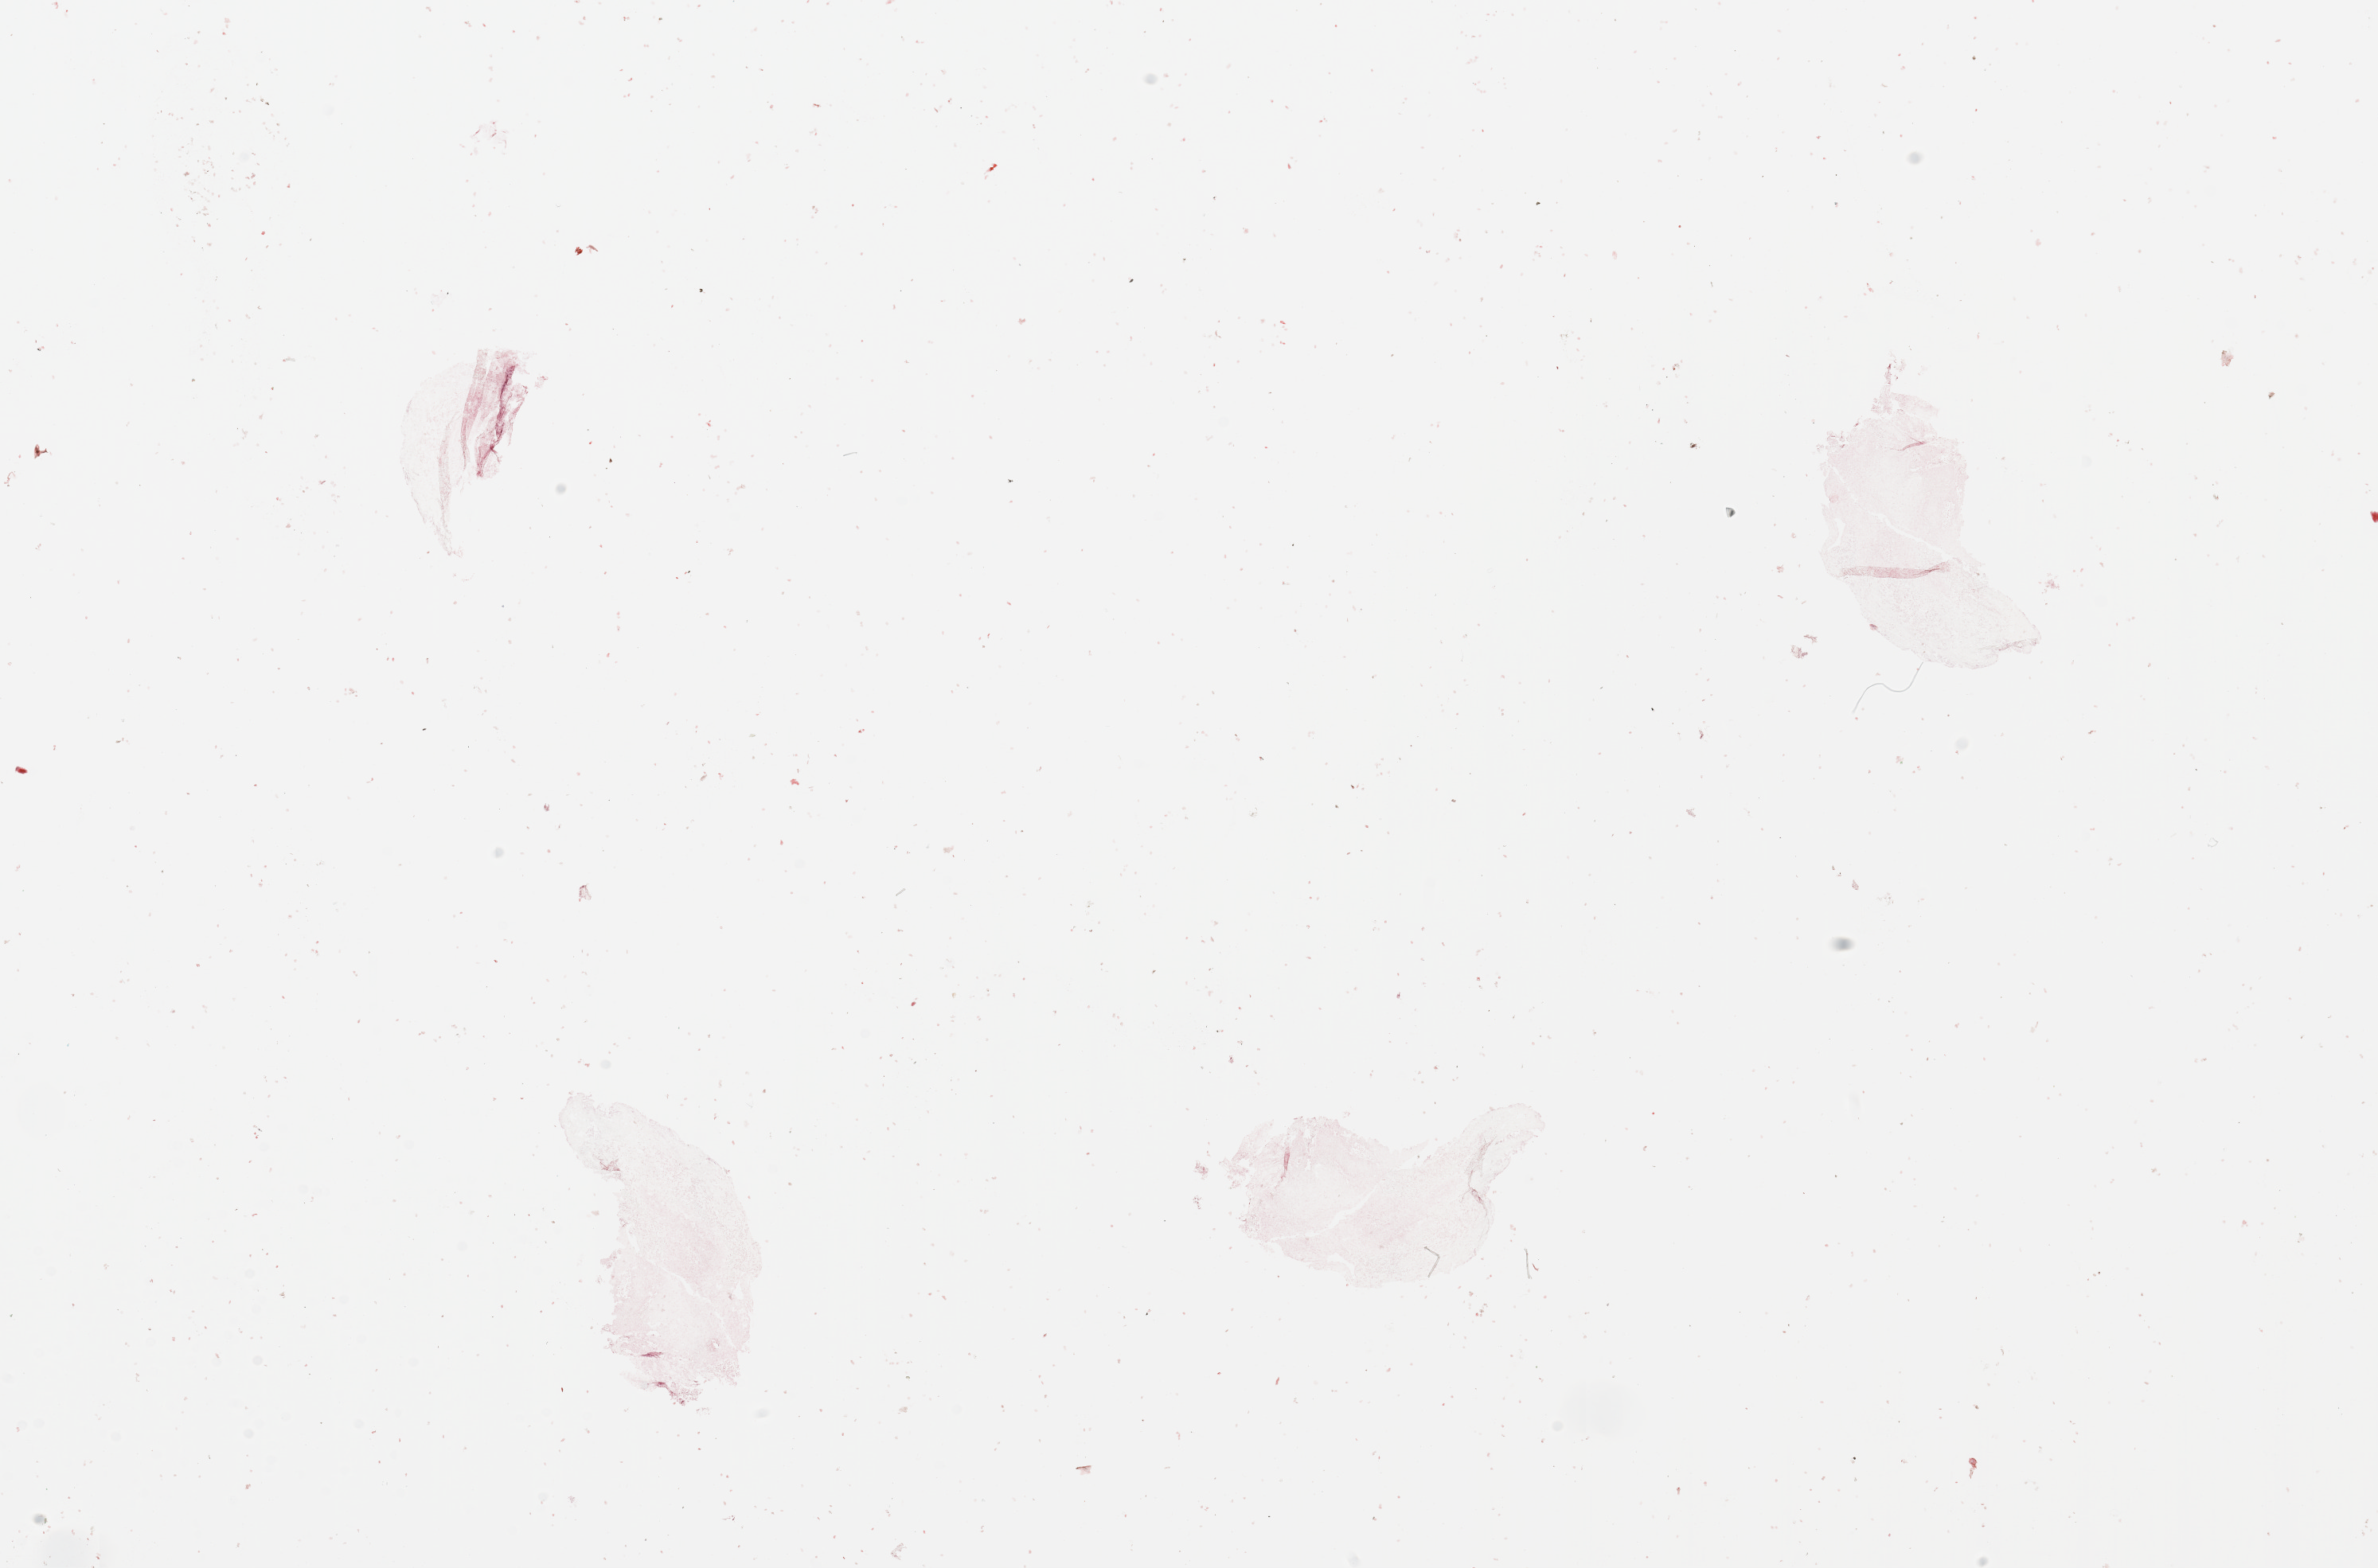
Hematoxylin and eosin (H&E) stained whole-slide image, a low-resolution overview of the entire scanned area, about 23.6 x 15.6 mm, head and neck, tissue type not recorded. Male, 64 y/o.
• patient diagnosis: Squamous cell carcinoma, NOS (larynx, NOS)